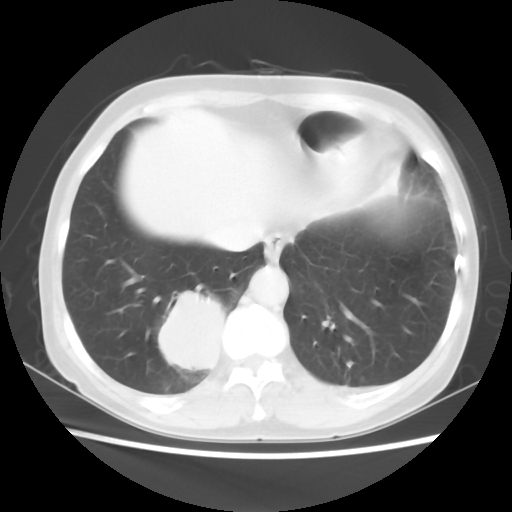
Chest CT, one axial slice; slice 13 of 56 in the series (ordered by position); reconstruction kernel STANDARD; 120 kVp; lung window (W 1500 / L -600 HU); 512 × 512 image matrix, field of view 332 × 332 mm. Patient: female, 66 years. Case-level facts recorded for this patient, not image findings: clinical TNM (as recorded): T2 N3 M0; histopathological grade: G3.
Outlined on this slice (rectangle marked by the reading radiologist):
- lung tumour (recorded histology: small cell carcinoma): bounding box (x1, y1, x2, y2) in pixels: (149, 283, 229, 376)